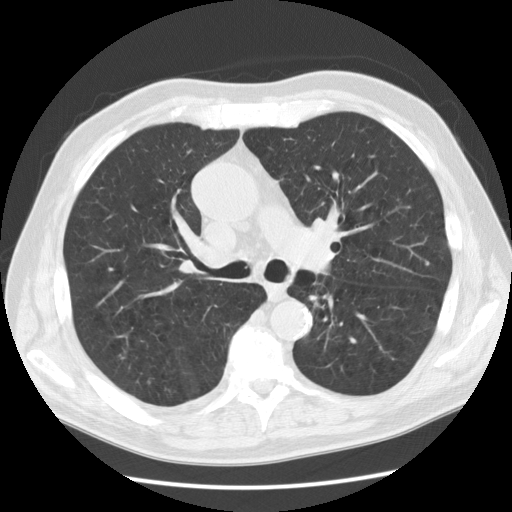
Low-dose screening chest CT, axial slice, second annual screen, lung window (W 1500 / L -600 HU), standard (soft-tissue) reconstruction kernel (STANDARD), 512 × 512 image matrix. Male, age 73 years at enrolment. Current smoker at enrolment.
Expert-annotated lung lesion, bounding box <293,275,339,317> (left, top, right, bottom; pixels). The screening reader recorded 4 non-calcified nodules or masses ≥4 mm on this exam; which of them this box marks is not recorded. Official screen result: positive, no significant change: stable abnormalities potentially related to lung cancer, unchanged since the prior screening exam. Later outcome: lung cancer diagnosed 302 days after this screen — small cell carcinoma, NOS, left lower lobe, stage IIIB (AJCC 6th edition), 55 mm at pathology.